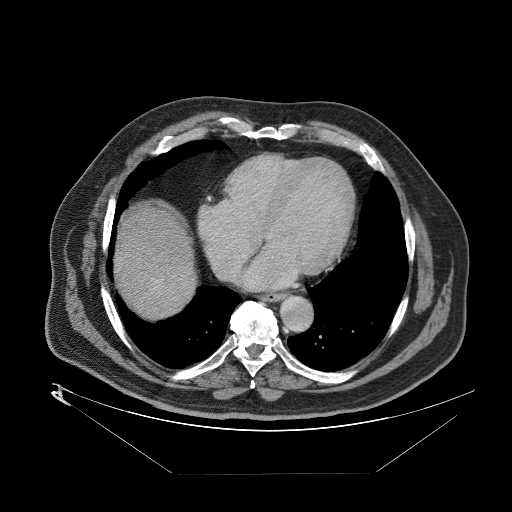
Contrast-enhanced abdominal CT (liver protocol), one axial slice; position 81 of 89 along the scan axis; one of 2 acquisitions stored at this slice position; soft-tissue window (W 400 / L 40 HU); 2.5 mm slice thickness; 512 × 512 image matrix. Case-level facts recorded for this patient, not image findings: diagnosis: hepatocellular carcinoma (patient treated with transarterial chemoembolisation; whether this scan precedes or follows treatment is not stated here); TNM stage (as recorded): Stage-II; Child-Pugh class: B; tumour differentiation: moderately differentiated; tumour size: 4 cm.
Annotated regions visible in this slice (semi-automatically segmented with operator editing):
- abdominal aorta: bounding box (x1, y1, x2, y2) in pixels: (277, 295, 312, 329)
- liver parenchyma outside the tumour (the mass and vessels are separate outlines, so this box may not span the whole liver): (118, 204, 186, 302)